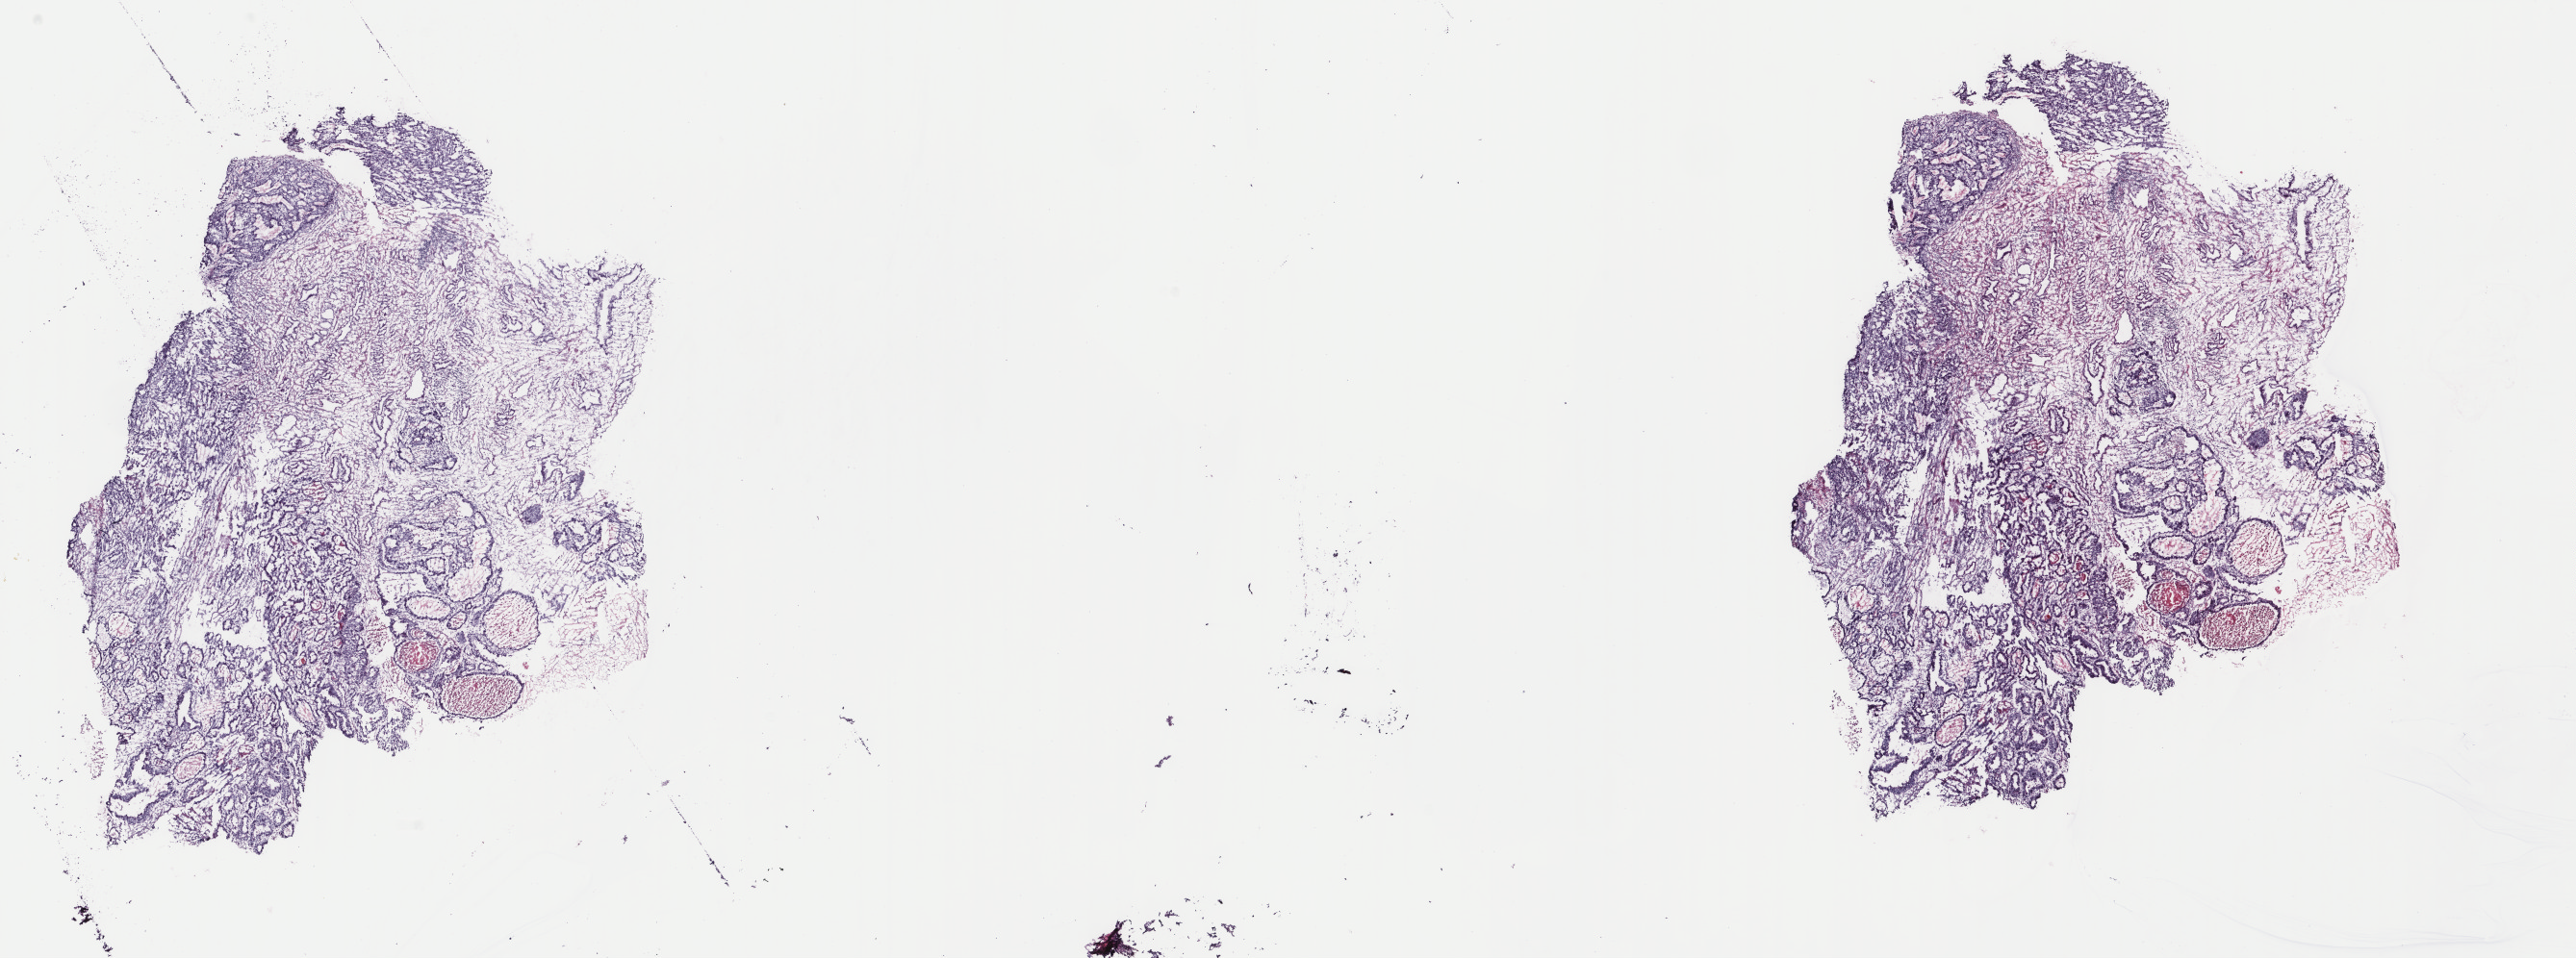
Hematoxylin and eosin (H&E) stained whole-slide image, low-resolution overview of the scanned area, about 21.2 x 7.9 mm; frozen section; sample: primary tumour, esophagus. Male, age 60 years at initial diagnosis. Histologic grade: GX (grade cannot be assessed). Composition of this section per pathologist review: tumour cells 70%, tumour nuclei 65%, normal cells 28%, stromal cells 0%, necrosis 2%. Inflammatory infiltration, as recorded: lymphocyte infiltration 0%, monocyte infiltration 0%, neutrophil infiltration 0%.
Diagnosis: Adenocarcinoma, NOS (lower third of esophagus). Lymph nodes positive (case pathology): 3 of 15 examined. AJCC pathologic stage: IIB (6th edition).